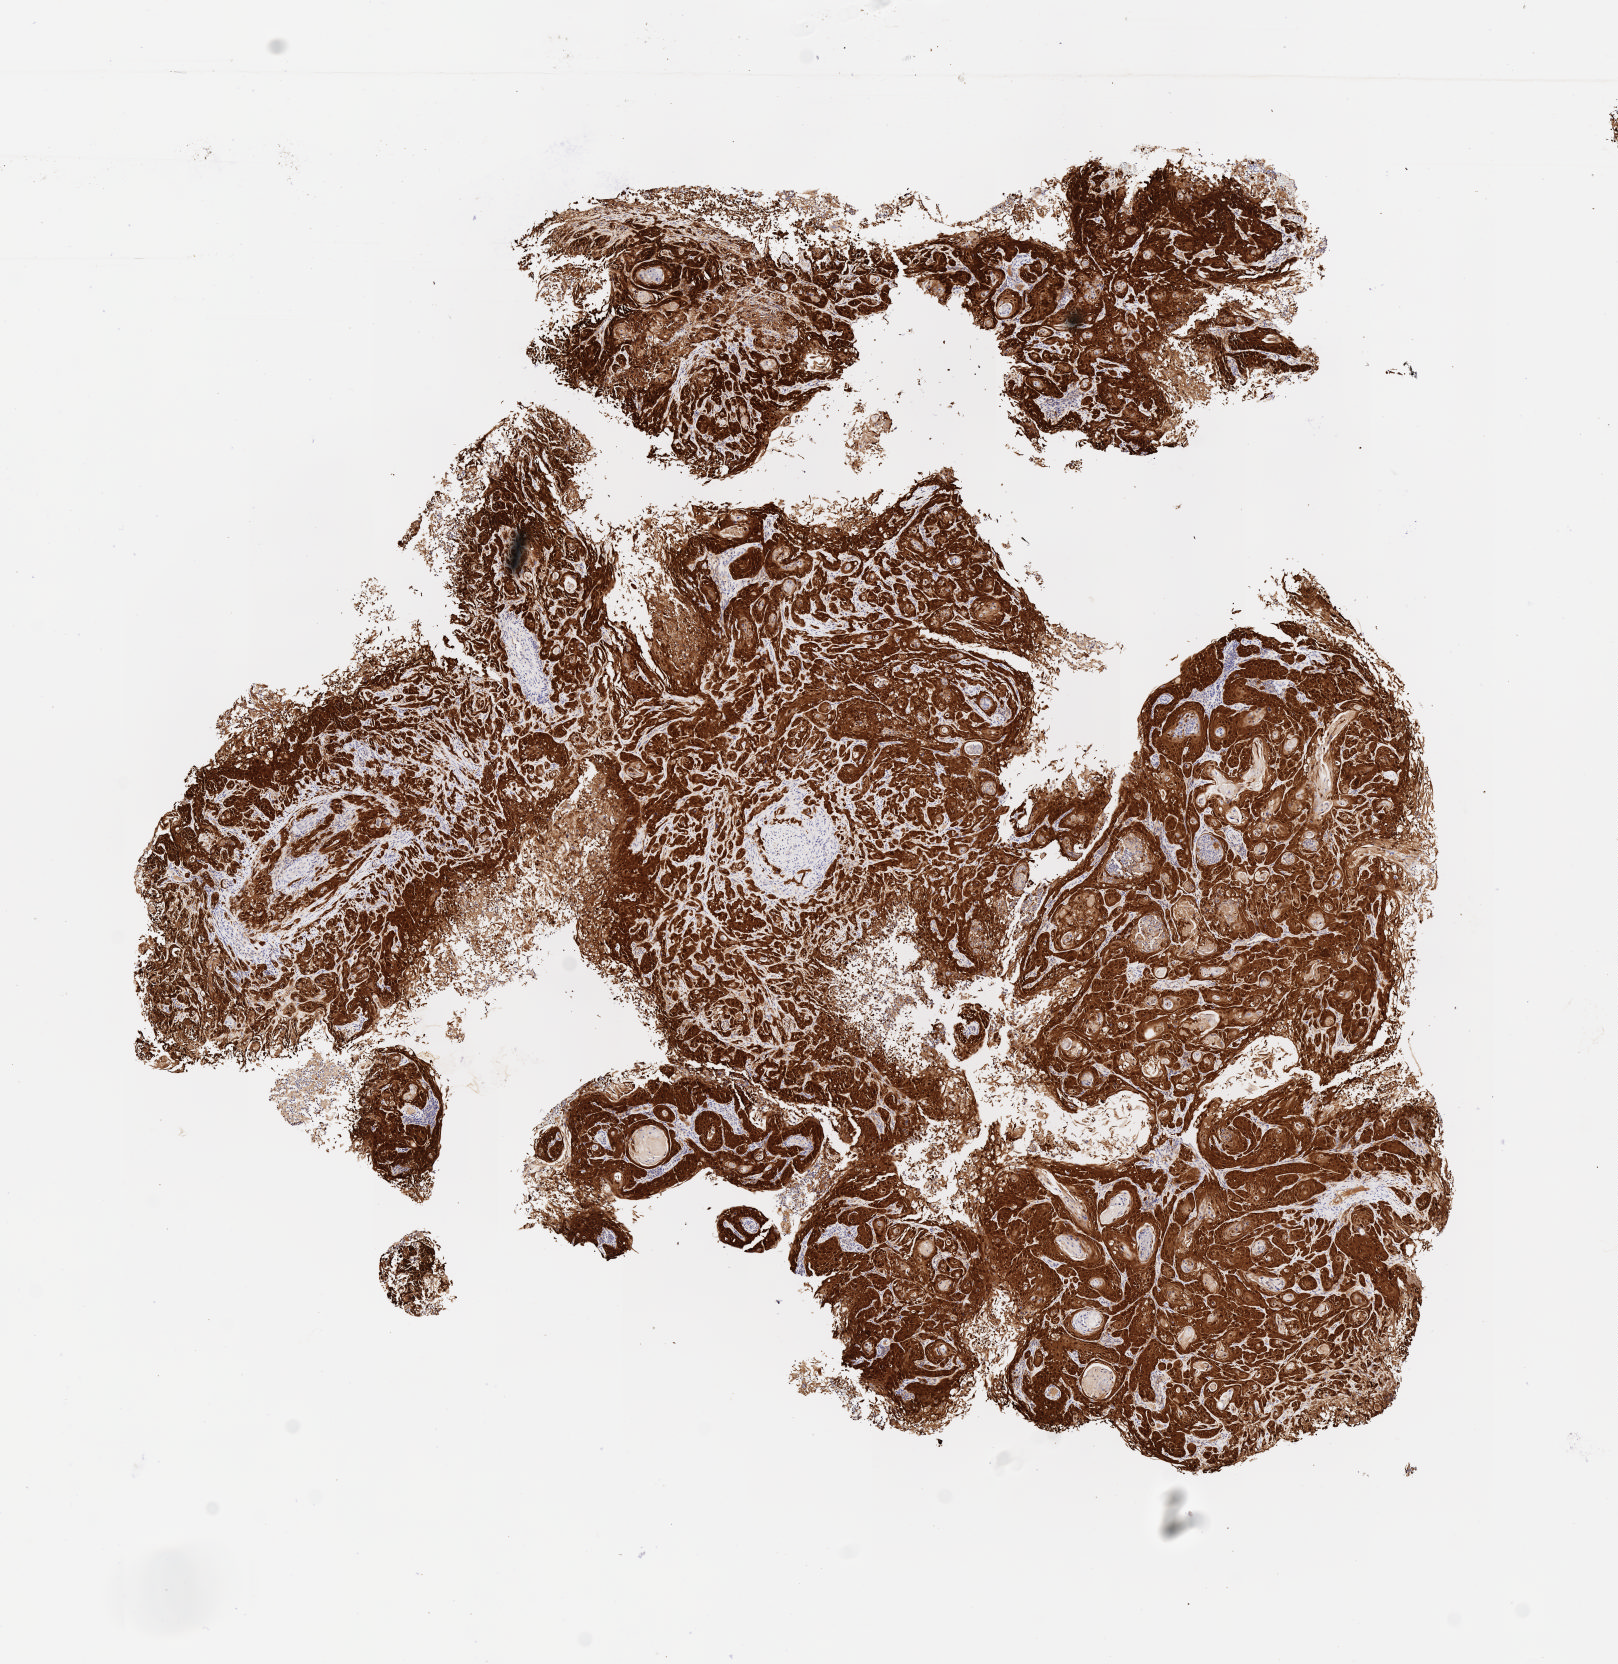
Immunohistochemistry (IHC) whole-slide image stained for p16 (p16INK4a) — low-resolution overview of the scanned area, about 6.5 x 6.7 mm, tumor tissue, site: cervix. Patient female; age 33 years.
Histologic diagnosis: Squamous cell carcinoma, keratinizing, NOS.